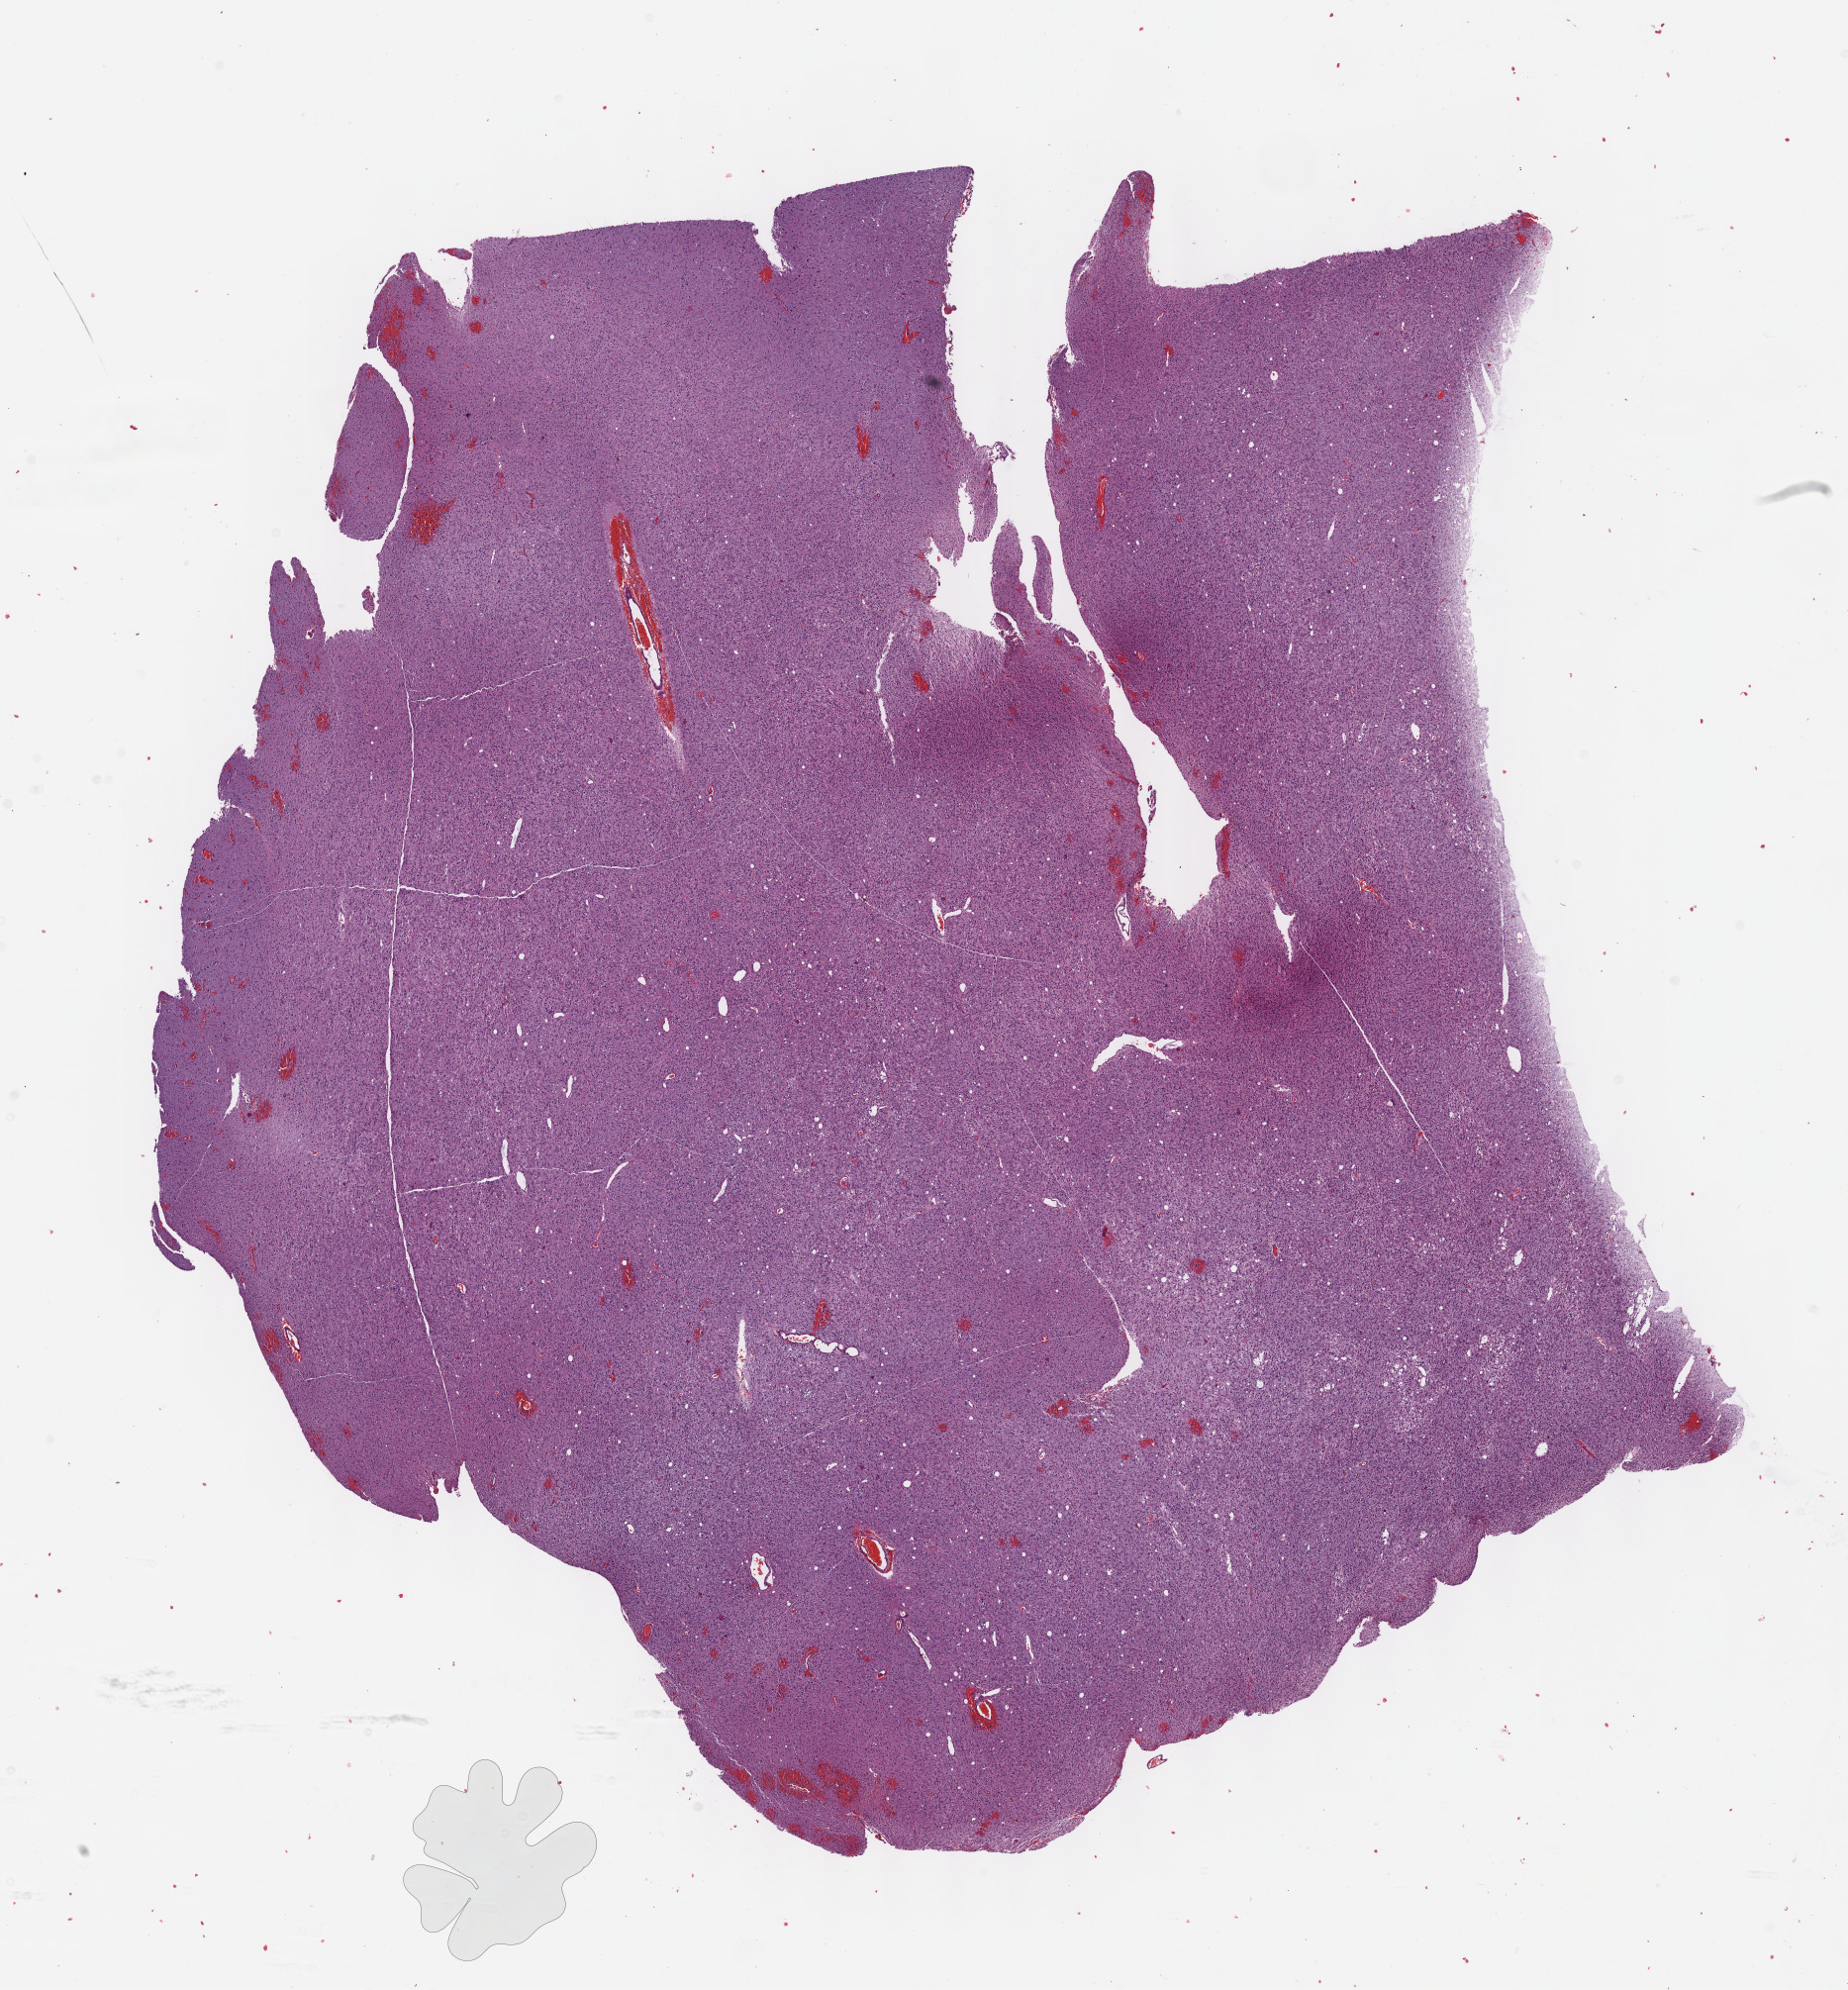
H&E-stained whole-slide image — low-resolution overview of the scanned area, about 15.1 x 16.2 mm (acquisition: 40x scan), formalin-fixed paraffin-embedded (FFPE) diagnostic section, sample: primary tumour, brain. Female patient; age at initial diagnosis 22 years.
Histologic diagnosis: Mixed glioma (cerebrum).